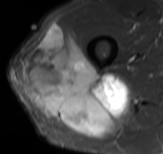
MRI of an extremity soft-tissue mass, one axial slice; slice 51 of 61 in the series (ordered by position); STIR; MR volume resampled by the dataset authors to the PET/CT grid (not the native acquisition matrix); 3.27 mm slice thickness; 163 × 154 image matrix. Male patient. From the clinical record (not read from this slice): histological type: poorly differentiated synovial sarcoma; grade: high; site of the primary tumour: right buttock.
Structures marked on this image (expert contour drawn on MRI and transferred to this co-registered scan by the dataset authors):
- gross tumour volume including surrounding oedema: box from (x=21, y=23) to (x=129, y=136) px
- gross tumour volume (mass): (x=21, y=23)–(x=129, y=136)